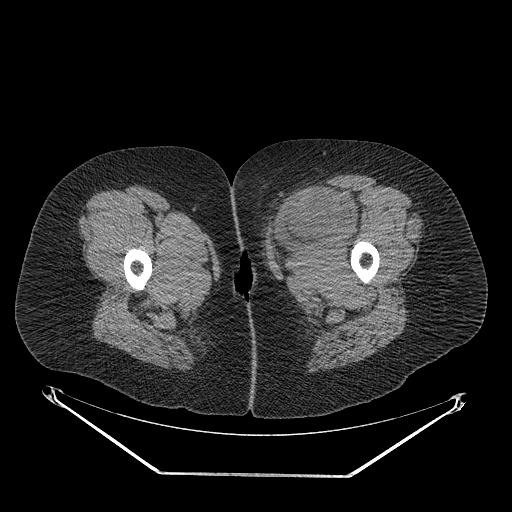
CT of an extremity soft-tissue mass (from a PET/CT study), one axial slice; slice 34 of 267 in the series (ordered by position); reconstruction kernel STANDARD; soft-tissue window (W 400 / L 40 HU); 3.75 mm slice thickness; 512 × 512 image matrix. Female patient. Case-level facts recorded for this patient, not image findings: histological type: myxofibrosarcoma; grade: intermediate; site of the primary tumour: left thigh.
Structures marked on this image (expert contour drawn on MRI and transferred to this co-registered scan by the dataset authors):
- gross tumour volume including surrounding oedema: bounding box (x1, y1, x2, y2) in pixels: (267, 187, 359, 261)
- gross tumour volume (mass): (269, 187, 355, 245)